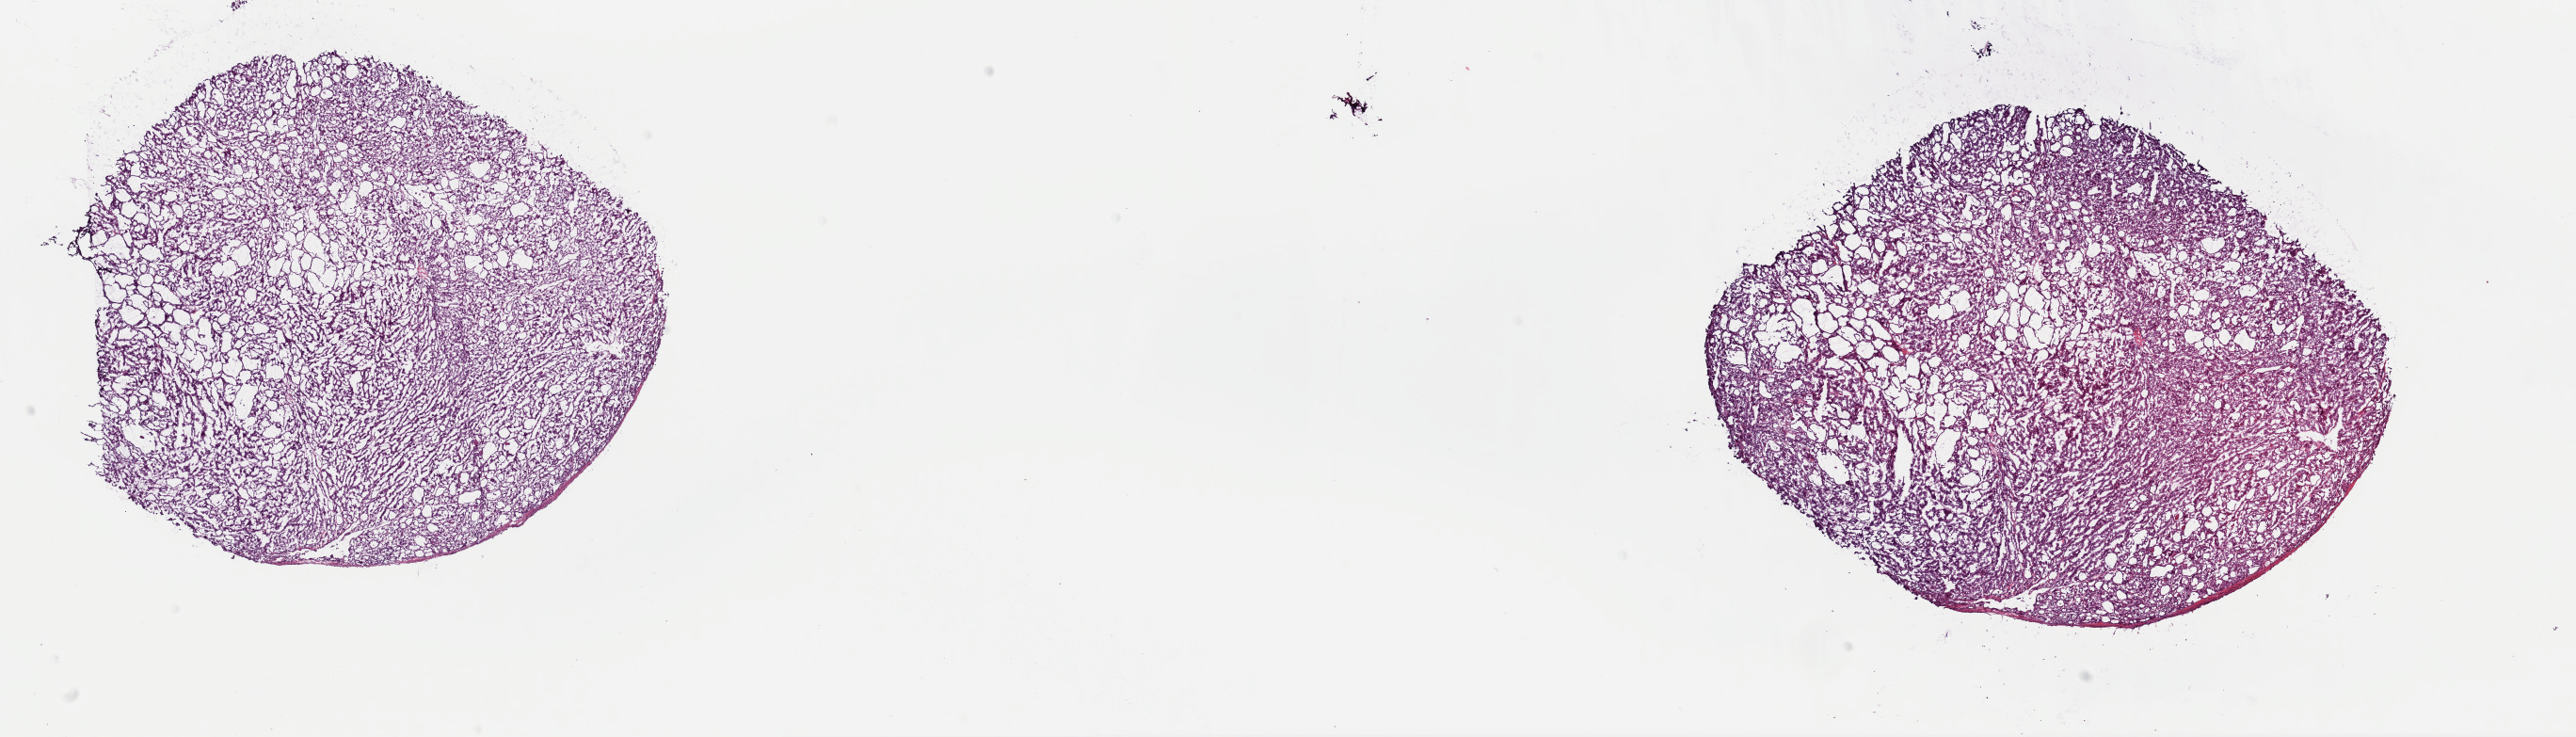
Hematoxylin and eosin (H&E) stained whole-slide image, whole scanned area (about 21.6 x 6.2 mm) shown as a low-resolution overview; frozen section from the top of the tissue portion; thyroid, primary tumour sample. Patient: male, age at initial diagnosis 38 years. Slide review estimates, as recorded: tumour cells 95%, tumour nuclei 100%, normal cells 0%, stromal cells 5%, necrosis 0%. Inflammatory infiltration, as recorded: lymphocyte infiltration 0%, monocyte infiltration 0%, neutrophil infiltration 0%.
• lymph nodes positive (case pathology): 0 of 1 examined
• histologic diagnosis: Papillary carcinoma, follicular variant
• AJCC pathologic stage: I (7th edition)